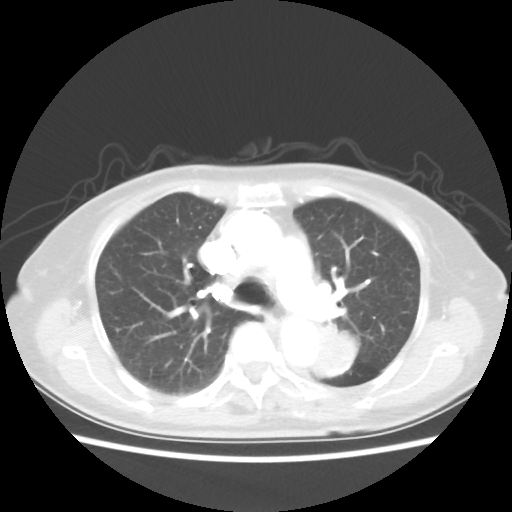
Chest CT, one axial slice. Position 32 of 50 along the scan axis. Lung window (W 1500 / L -600 HU). 5 mm slice thickness. 512 × 512 image matrix, field of view 335 × 335 mm. Female patient, age 81 years. From the clinical record (not read from this slice): clinical TNM (as recorded): T2 N0 M1a.
Outlined on this slice (rectangle marked by the reading radiologist):
- lung tumour (recorded histology: squamous cell carcinoma): box from (x=312, y=320) to (x=357, y=379) px